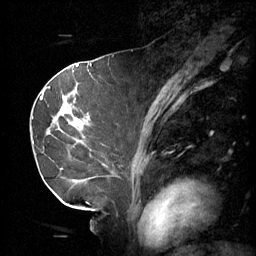
Breast MRI (dynamic contrast-enhanced), one sagittal slice; slice 29 of 60 in the series (ordered by position); 3 images stored at this slice position (order not interpretable as contrast timing); 1.5 T; TE 4.2 ms, TR 11 ms; 2 mm slice thickness; 256 × 256 image matrix, field of view 220 × 220 mm. Female patient, age 69 years.
Annotated regions visible in this slice (semi-automatic segmentation, software-assisted and operator-edited):
- analysis volume of interest (the breast-tissue region the enhancement analysis was run in; not a lesion): bounding box [x1, y1, x2, y2] px = [36, 88, 112, 189]
- tumour enhancement mask (voxels above the 70 % enhancement threshold inside the analysis volume of interest): [40, 92, 88, 137]